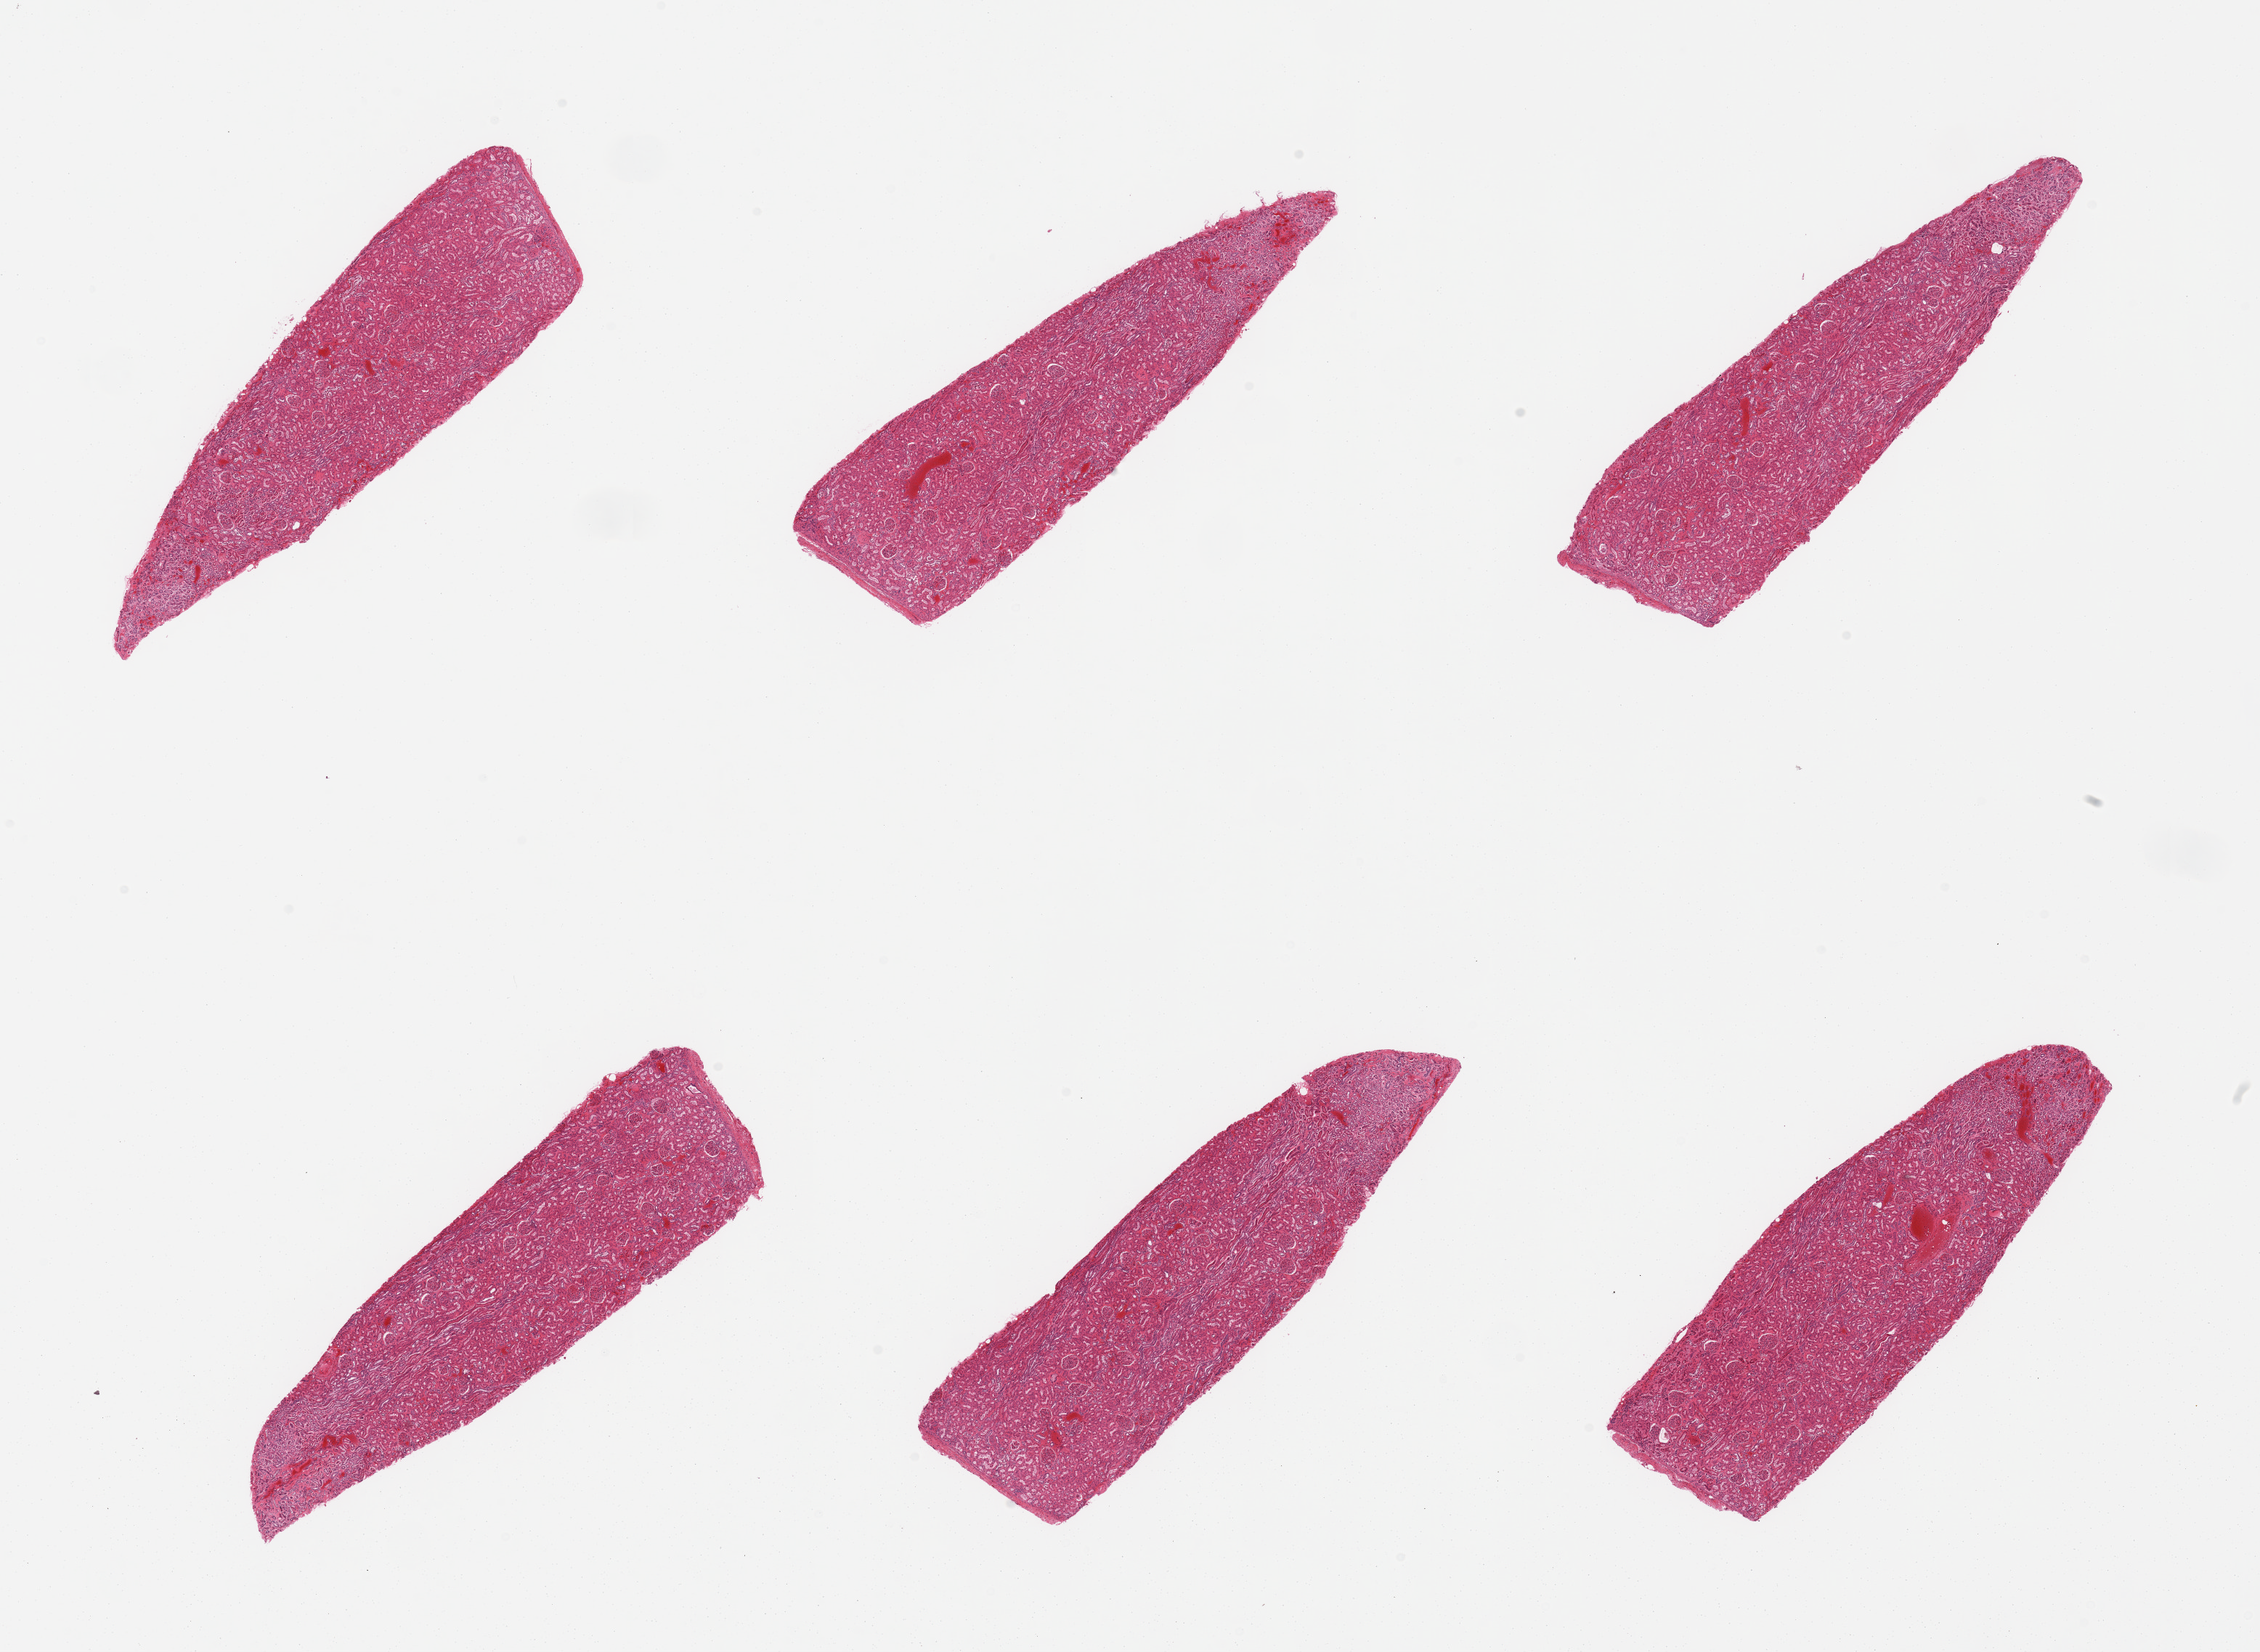
Whole-slide image, hematoxylin and eosin (H&E) stain — shown as a low-resolution overview of the whole scanned area (about 24.6 x 18.0 mm, acquisition: 20x scan); PAXgene-fixed paraffin-embedded (PFPE) section; target tissue: renal cortex; tissue donor sample. Donor sex: female.
Reviewer comment on this tissue sample: 6 pieces, glomeruli in all sections, rare sclerotic glomerulus, focal vascular hyalinization/thickening.